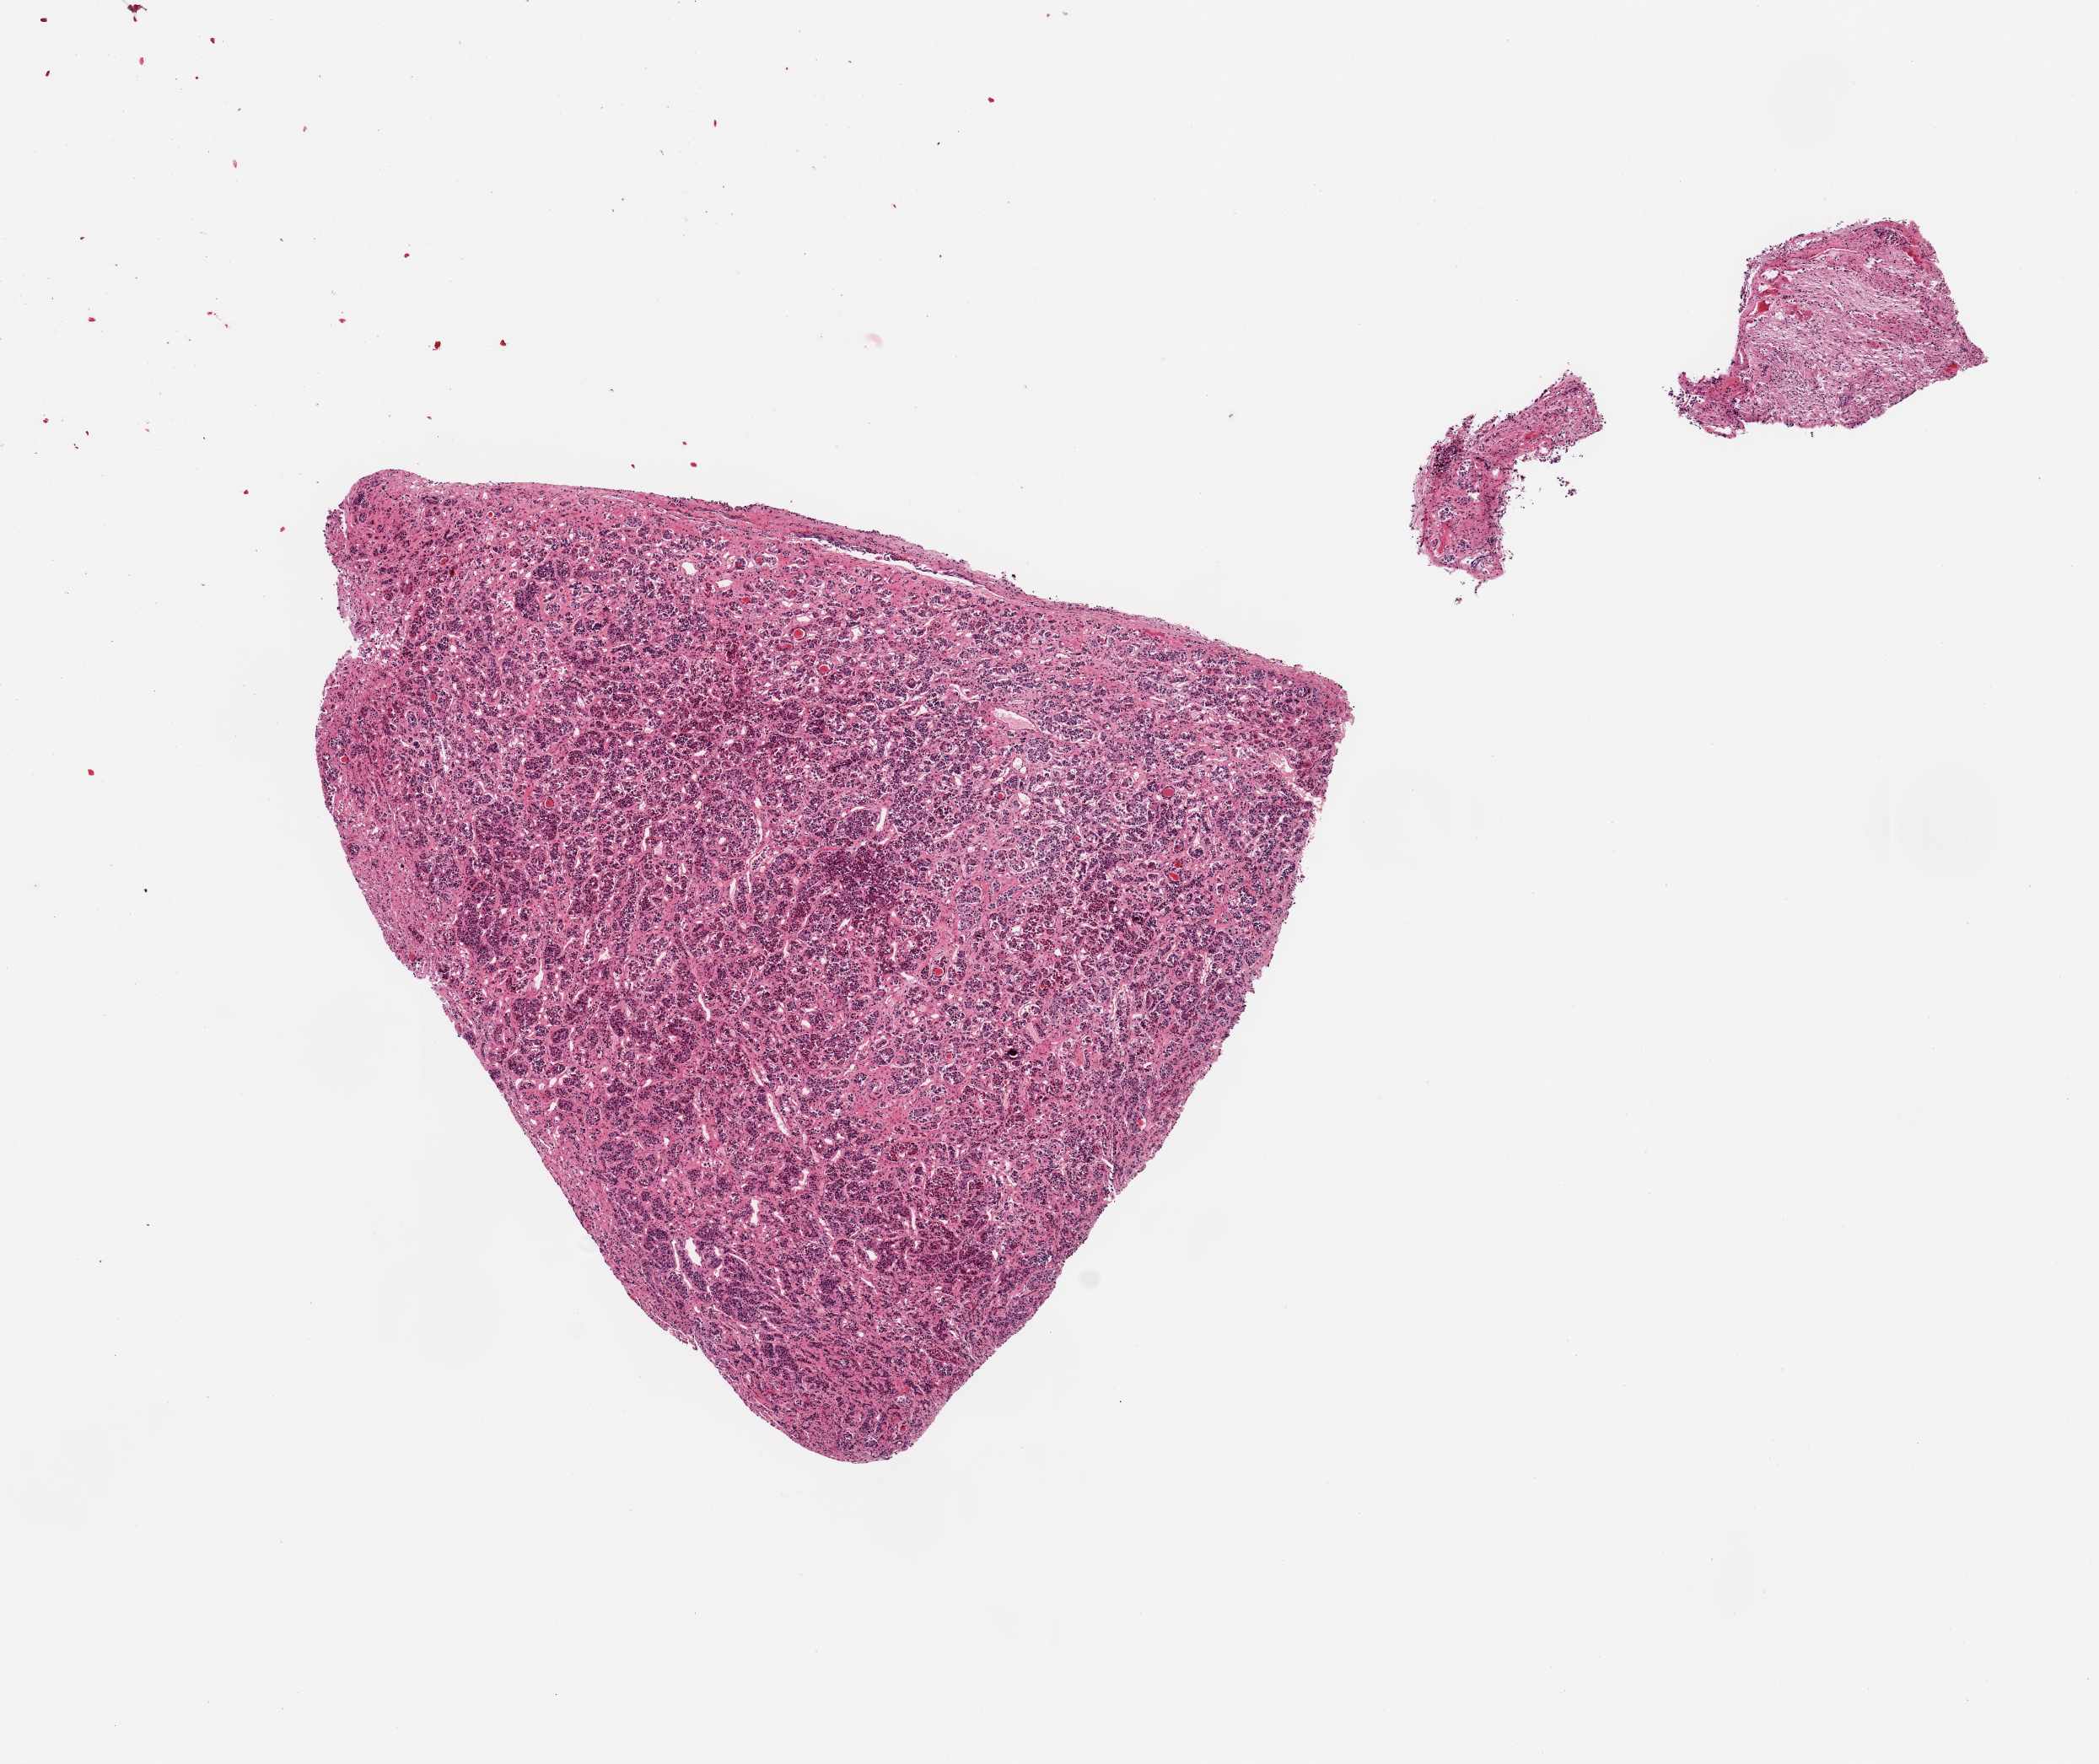
Whole-slide image, haematoxylin and eosin stain, a low-resolution overview of the entire scanned area, about 9.8 x 8.3 mm; PAXgene-fixed, paraffin-embedded tissue; sampled site (target tissue): pituitary; tissue donor sample. Donor sex: female.
- review note (as recorded): 2 pieces; 4.7mm anterior lobe; 0.8mm posterior lobe fragment